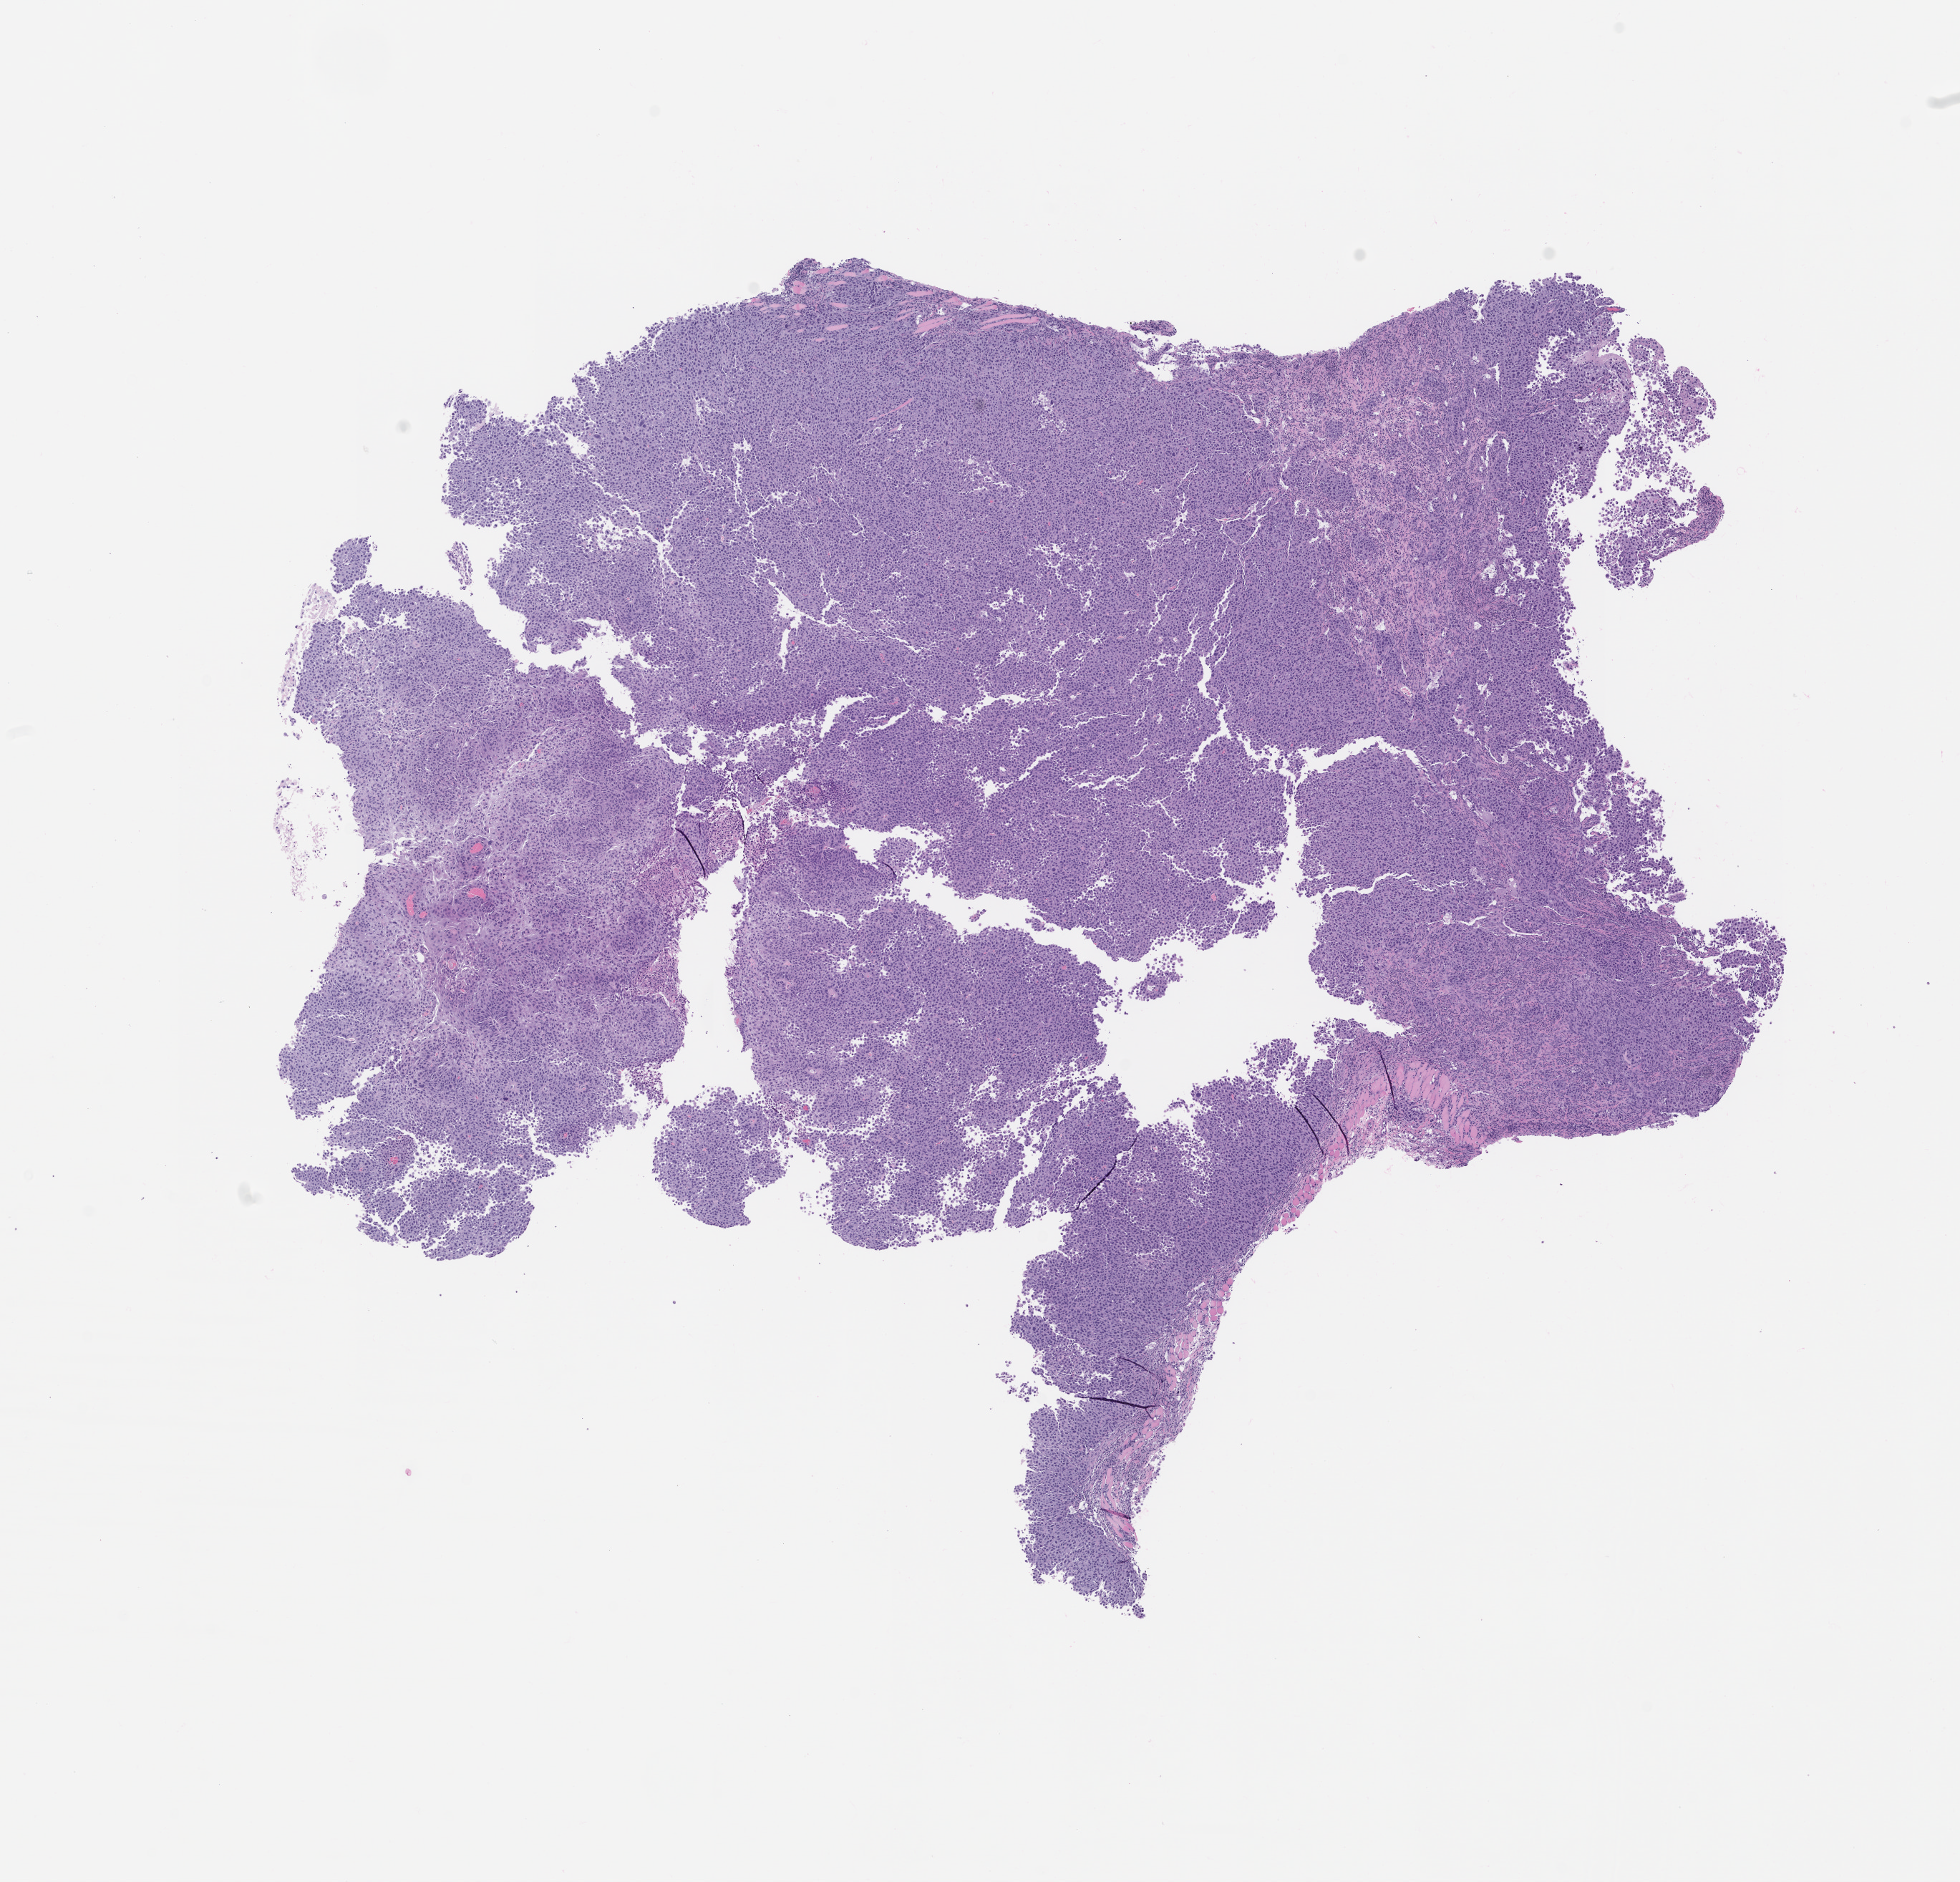
H&E whole-slide image of a patient-derived xenograft (PDX) tumor grown in a mouse, passage 1, low-resolution overview of the scanned area, about 11.0 x 10.5 mm, formalin-fixed, paraffin-embedded (FFPE) tissue, tumor site category: head and neck.
Originating patient diagnosis: Head and Neck Squamous Cell Carcinoma.